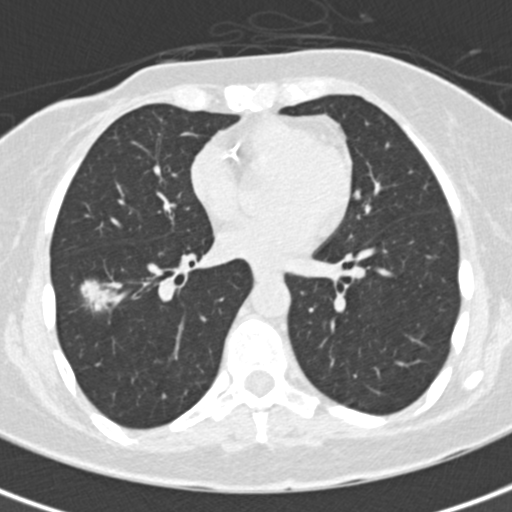
Low-dose screening chest CT, axial slice, baseline screening round, lung window (W 1500 / L -600 HU), 2 mm slice thickness, standard (soft-tissue) reconstruction kernel (B30f), slice 94 of 171 in the series. Female participant, aged 56 years at enrolment.
Expert reader's lesion annotation, bounding box <71,274,130,329> (left, top, right, bottom; pixels). The screening reader recorded 5 non-calcified nodules or masses ≥4 mm on this exam (right lower lobe, right upper lobe, left upper lobe, left lower lobe, left lower lobe); which of them this box marks is not recorded. Official screen result: positive, change unspecified: nodule(s) >= 4 mm or enlarging nodule(s), mass(es), or other non-specific abnormalities suspicious for lung cancer. Later outcome: lung cancer diagnosed 26 days after this screen — bronchiolo-alveolar carcinoma, mucinous, right lower lobe, well differentiated (G1), stage IA (AJCC 6th edition), 19 mm at pathology.